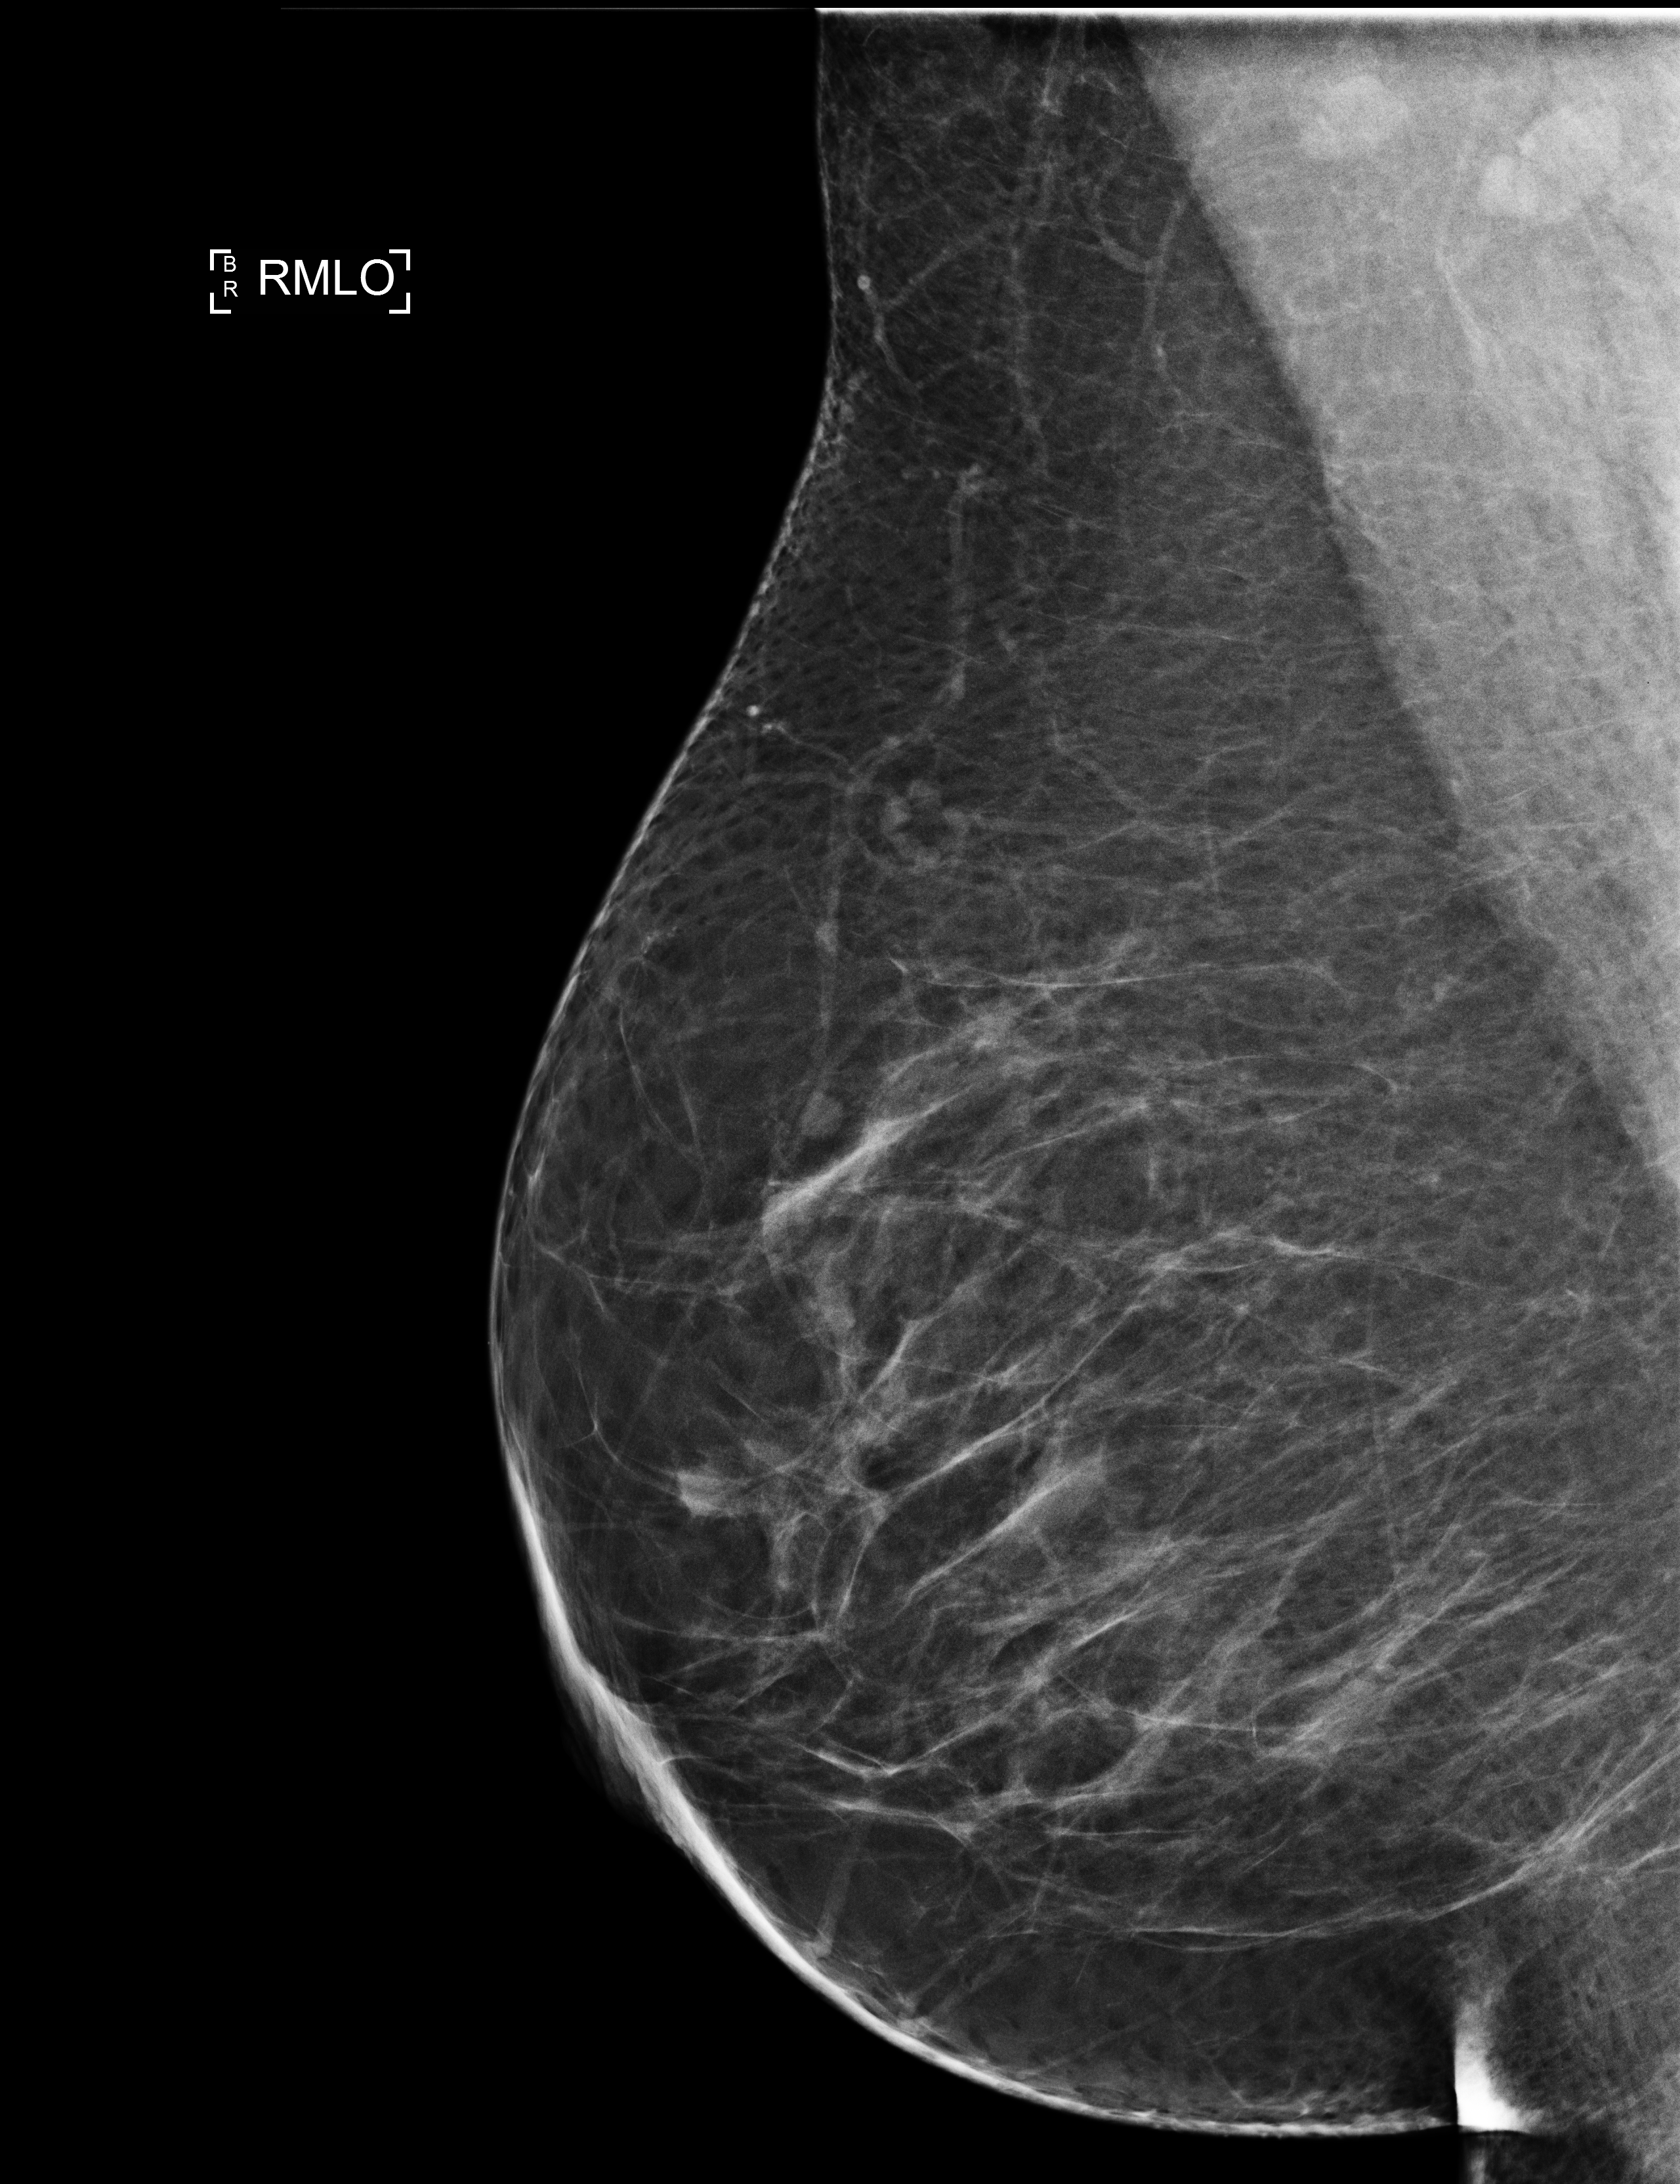
Digital mammogram (FFDM), right breast, mediolateral oblique (MLO) view, screening examination, system: Selenia Dimensions. Female patient, age 44 years.
BI-RADS breast density category at the screening exam (both breasts, scale 1–4): 2. Final BI-RADS assessment for this screening round (tomosynthesis exam, both breasts): category 2. Recall: no recall after this screen.